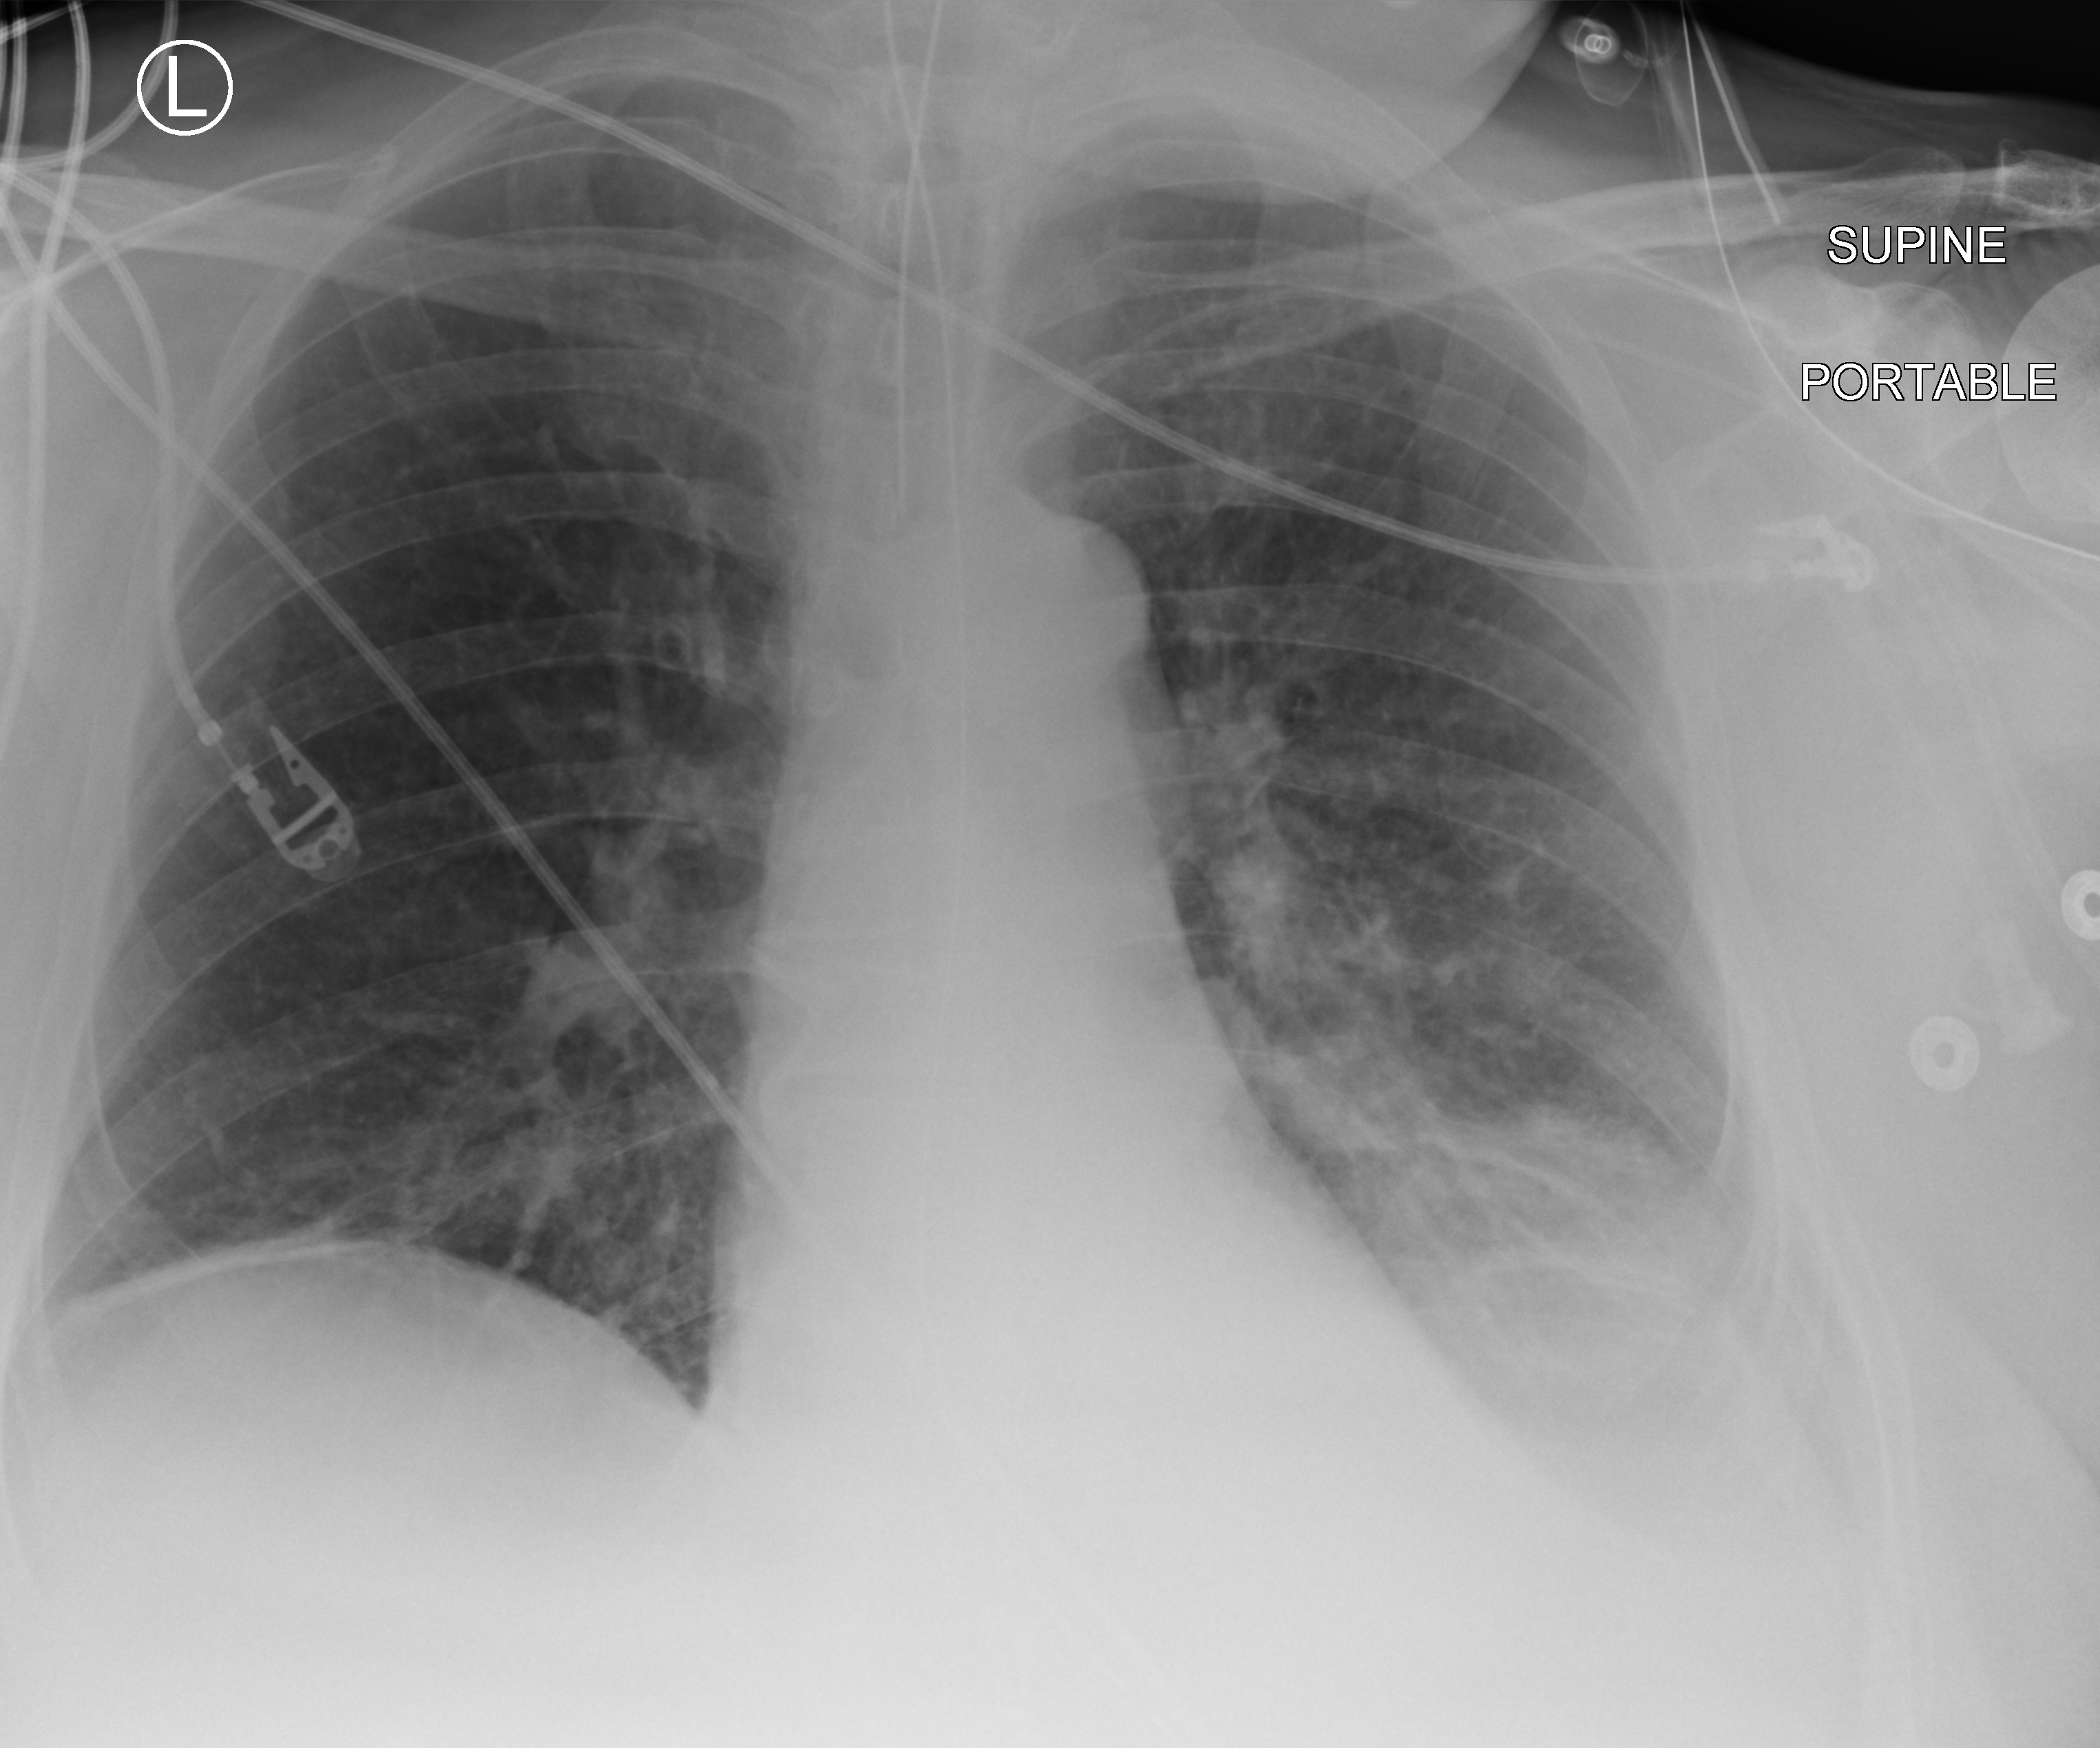
Portable chest radiograph, anteroposterior (AP) projection. Patient hospitalised with COVID-19; male, aged 60–74 years.
From the hospital-stay record, not from the radiograph (when in the stay this image was taken is not recorded):
- mechanically ventilated during this hospital stay: yes
- admitted to intensive care during this hospital stay: yes
- other chronic lung disease (admission record): no